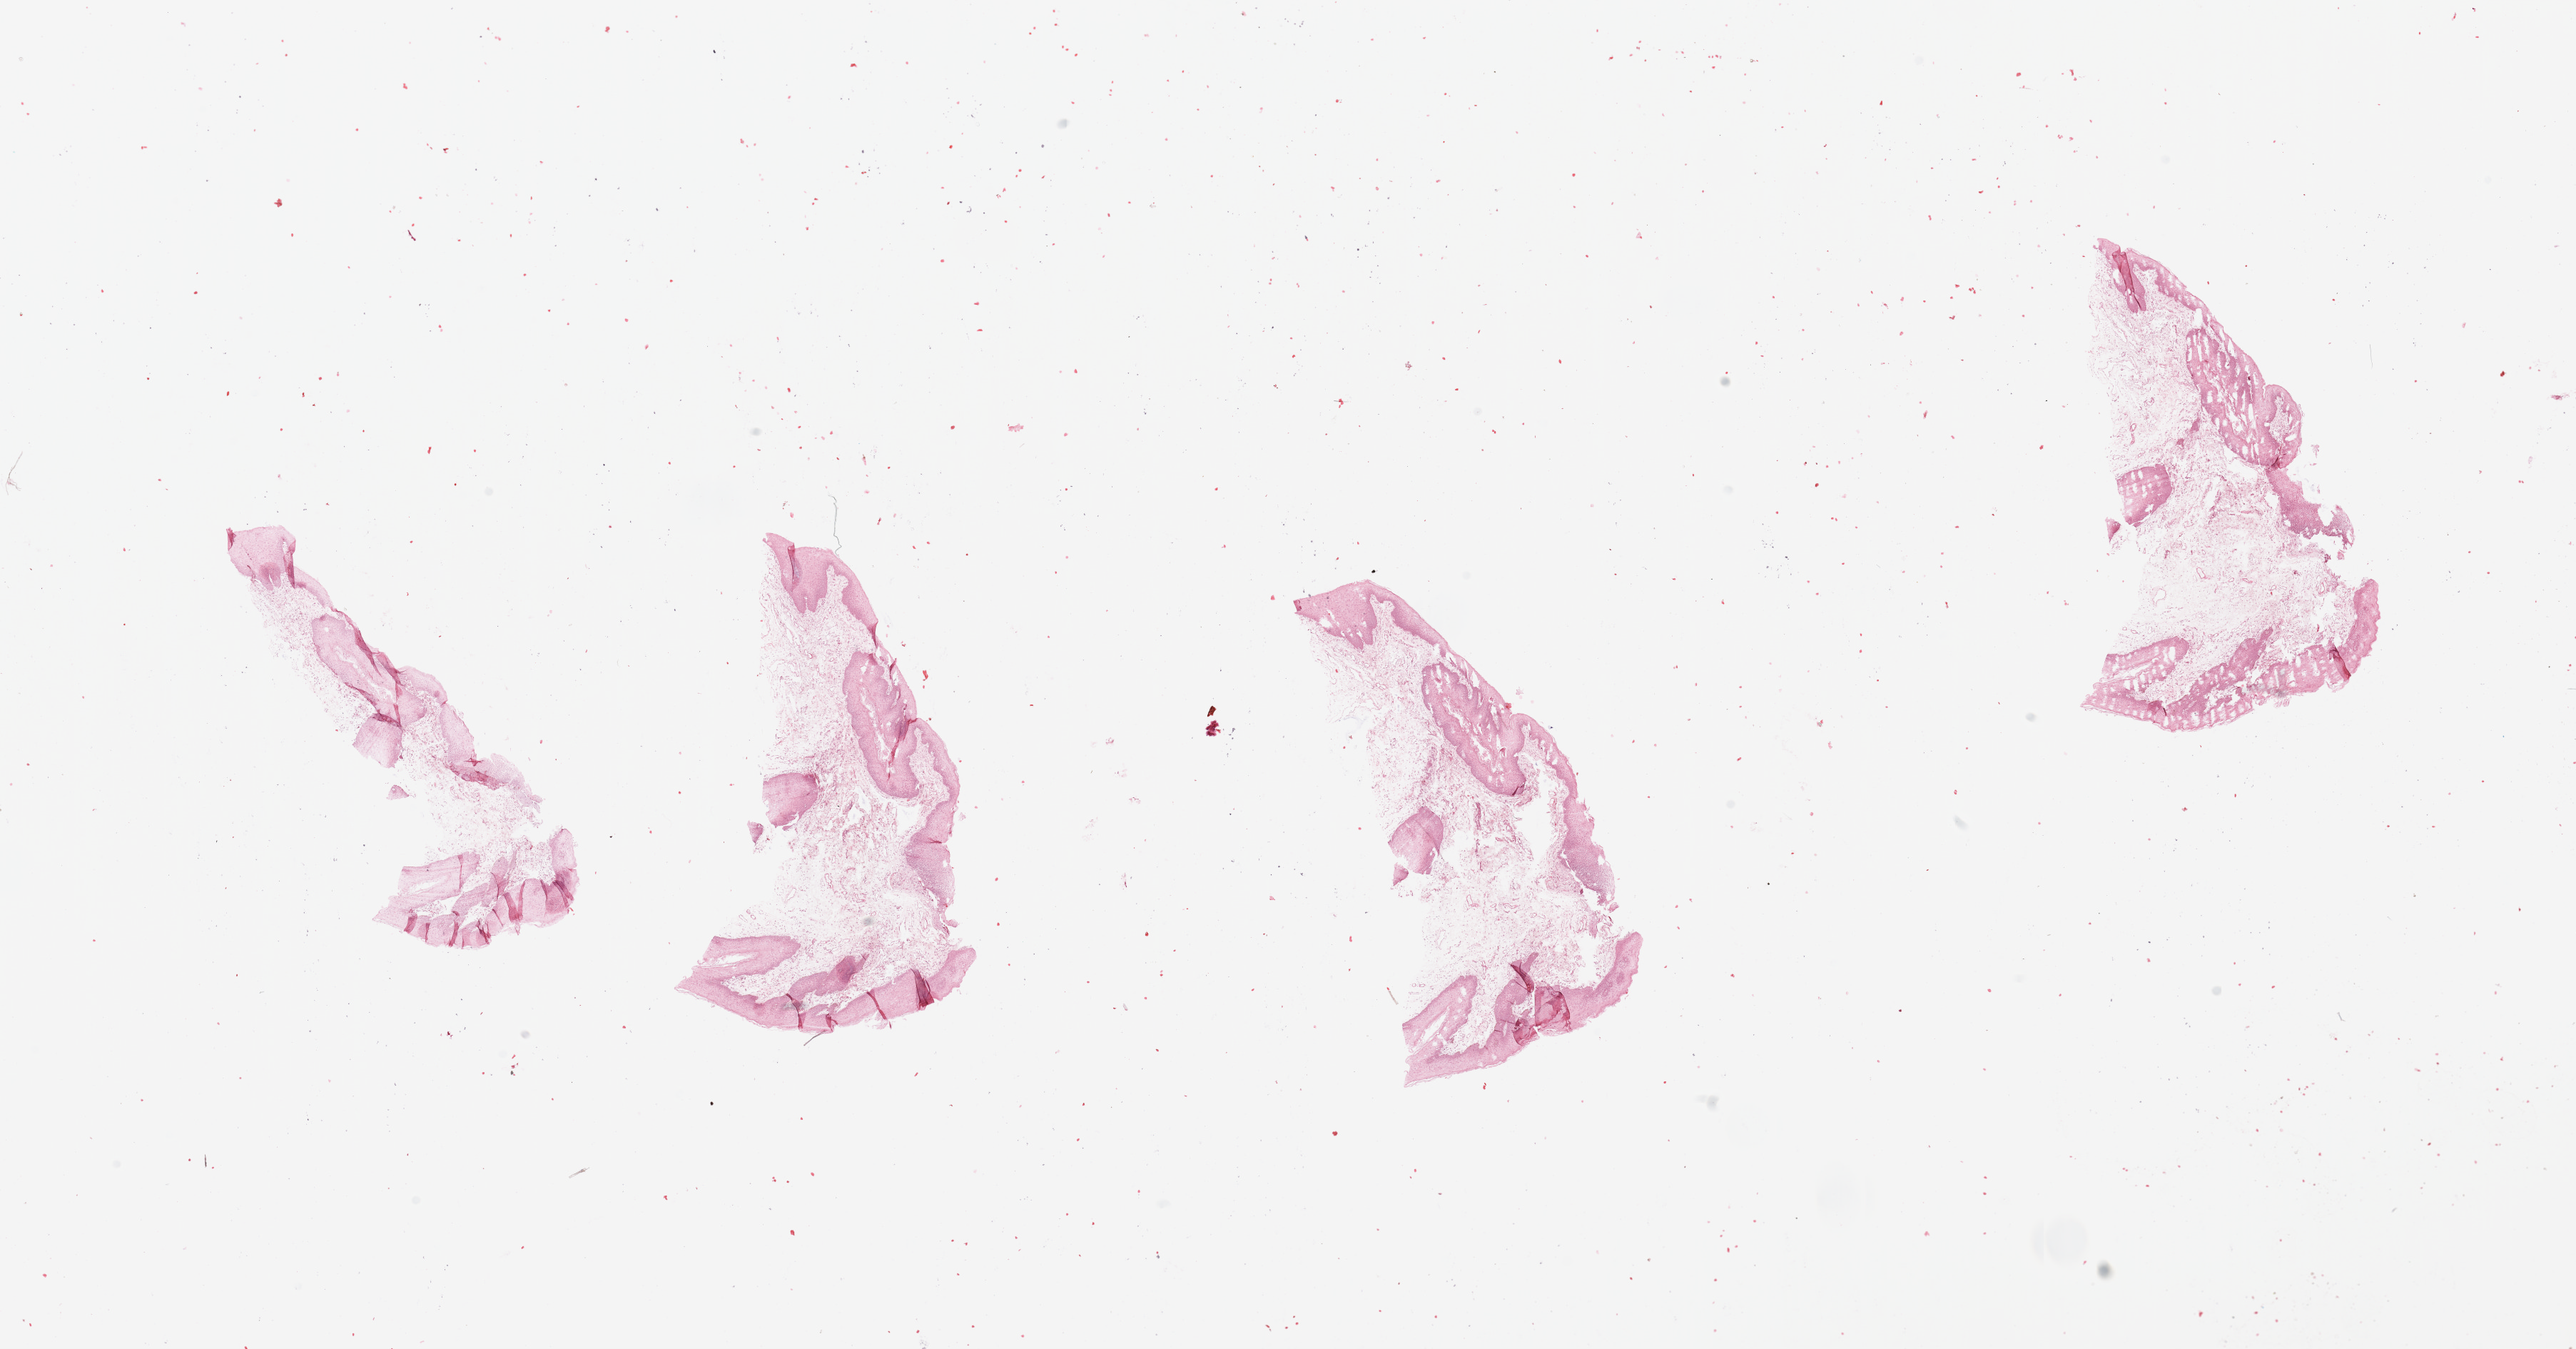
Digitized Hematoxylin and eosin (H&E) stained tissue section (whole slide) — a low-resolution overview of the entire scanned area, about 28.5 x 14.9 mm (slide scanned at 20x). Normal (non-tumour) tissue sample, sampled site: floor of mouth. Patient: male, age 65 years.
This section: normal (non-tumour) tissue from the same patient. Patient diagnosis: Squamous cell carcinoma, NOS (floor of mouth, NOS).